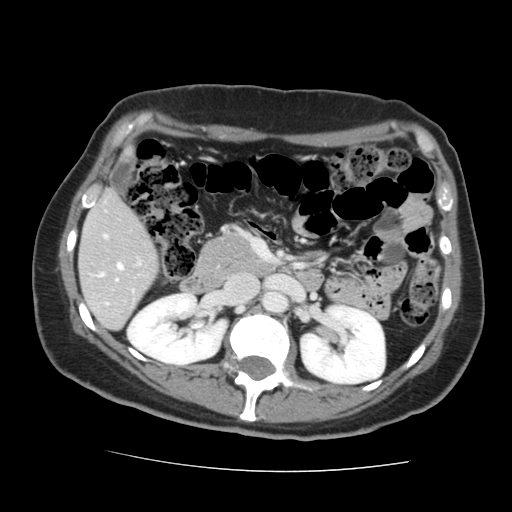
Contrast-enhanced abdominal CT, one axial slice; slice 69 of 144 in the series (ordered by position); 120 kVp; soft-tissue window (W 400 / L 40 HU); 2.5 mm slice thickness; 512 × 512 image matrix. Female patient, age 46 years. From the clinical record (not read from this slice): diagnosis: colorectal cancer liver metastases, imaged before liver resection; multiple liver metastases: no; largest metastasis: 2.8 cm.
Structures marked on this image (outlined manually by an expert reader):
- liver: bounding box <80,193,158,329> (left, top, right, bottom; pixels)
- planned liver remnant (the part of the liver to remain after resection): <80,193,158,317>
- portal vein (with intrahepatic branches): <98,235,140,281>